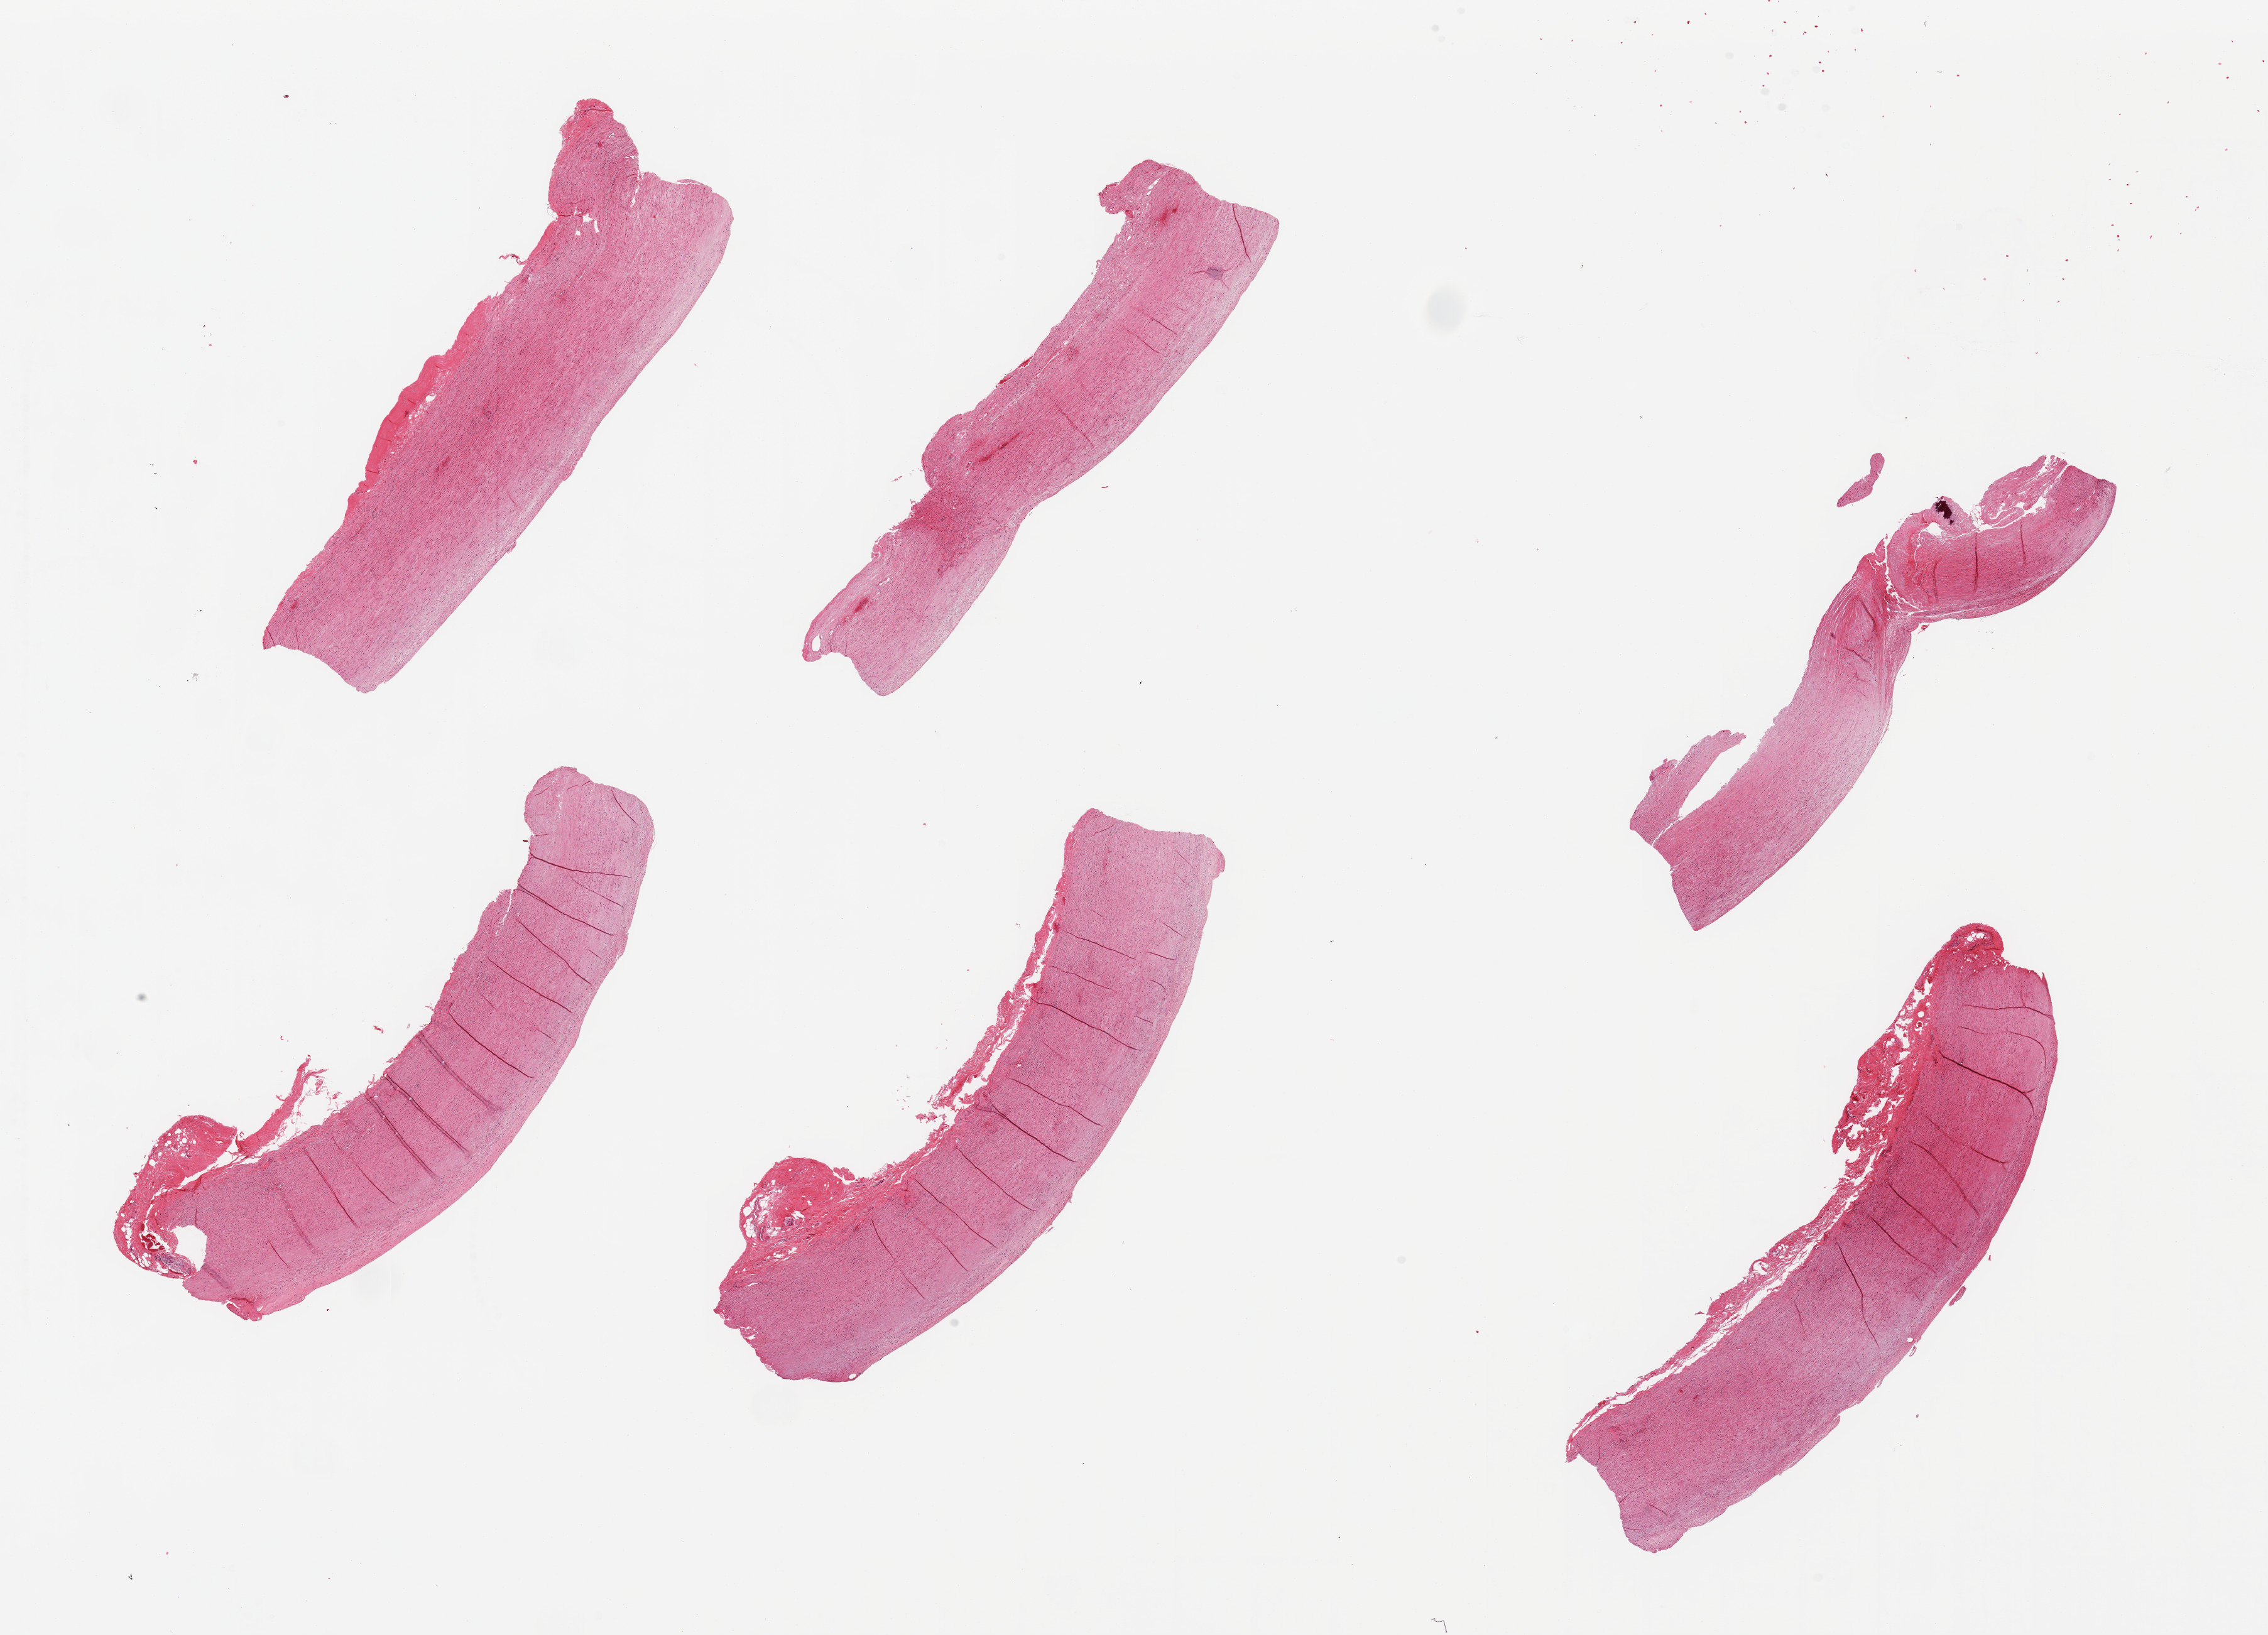
Digitized haematoxylin and eosin-stained section, brightfield, a low-resolution overview of the entire scanned area, about 28.5 x 20.6 mm. PAXgene-fixed paraffin-embedded (PFPE) section. Target tissue: aorta. Tissue donor sample. Male donor.
Review note (as recorded): 6 pieces; flat intimal plaques.